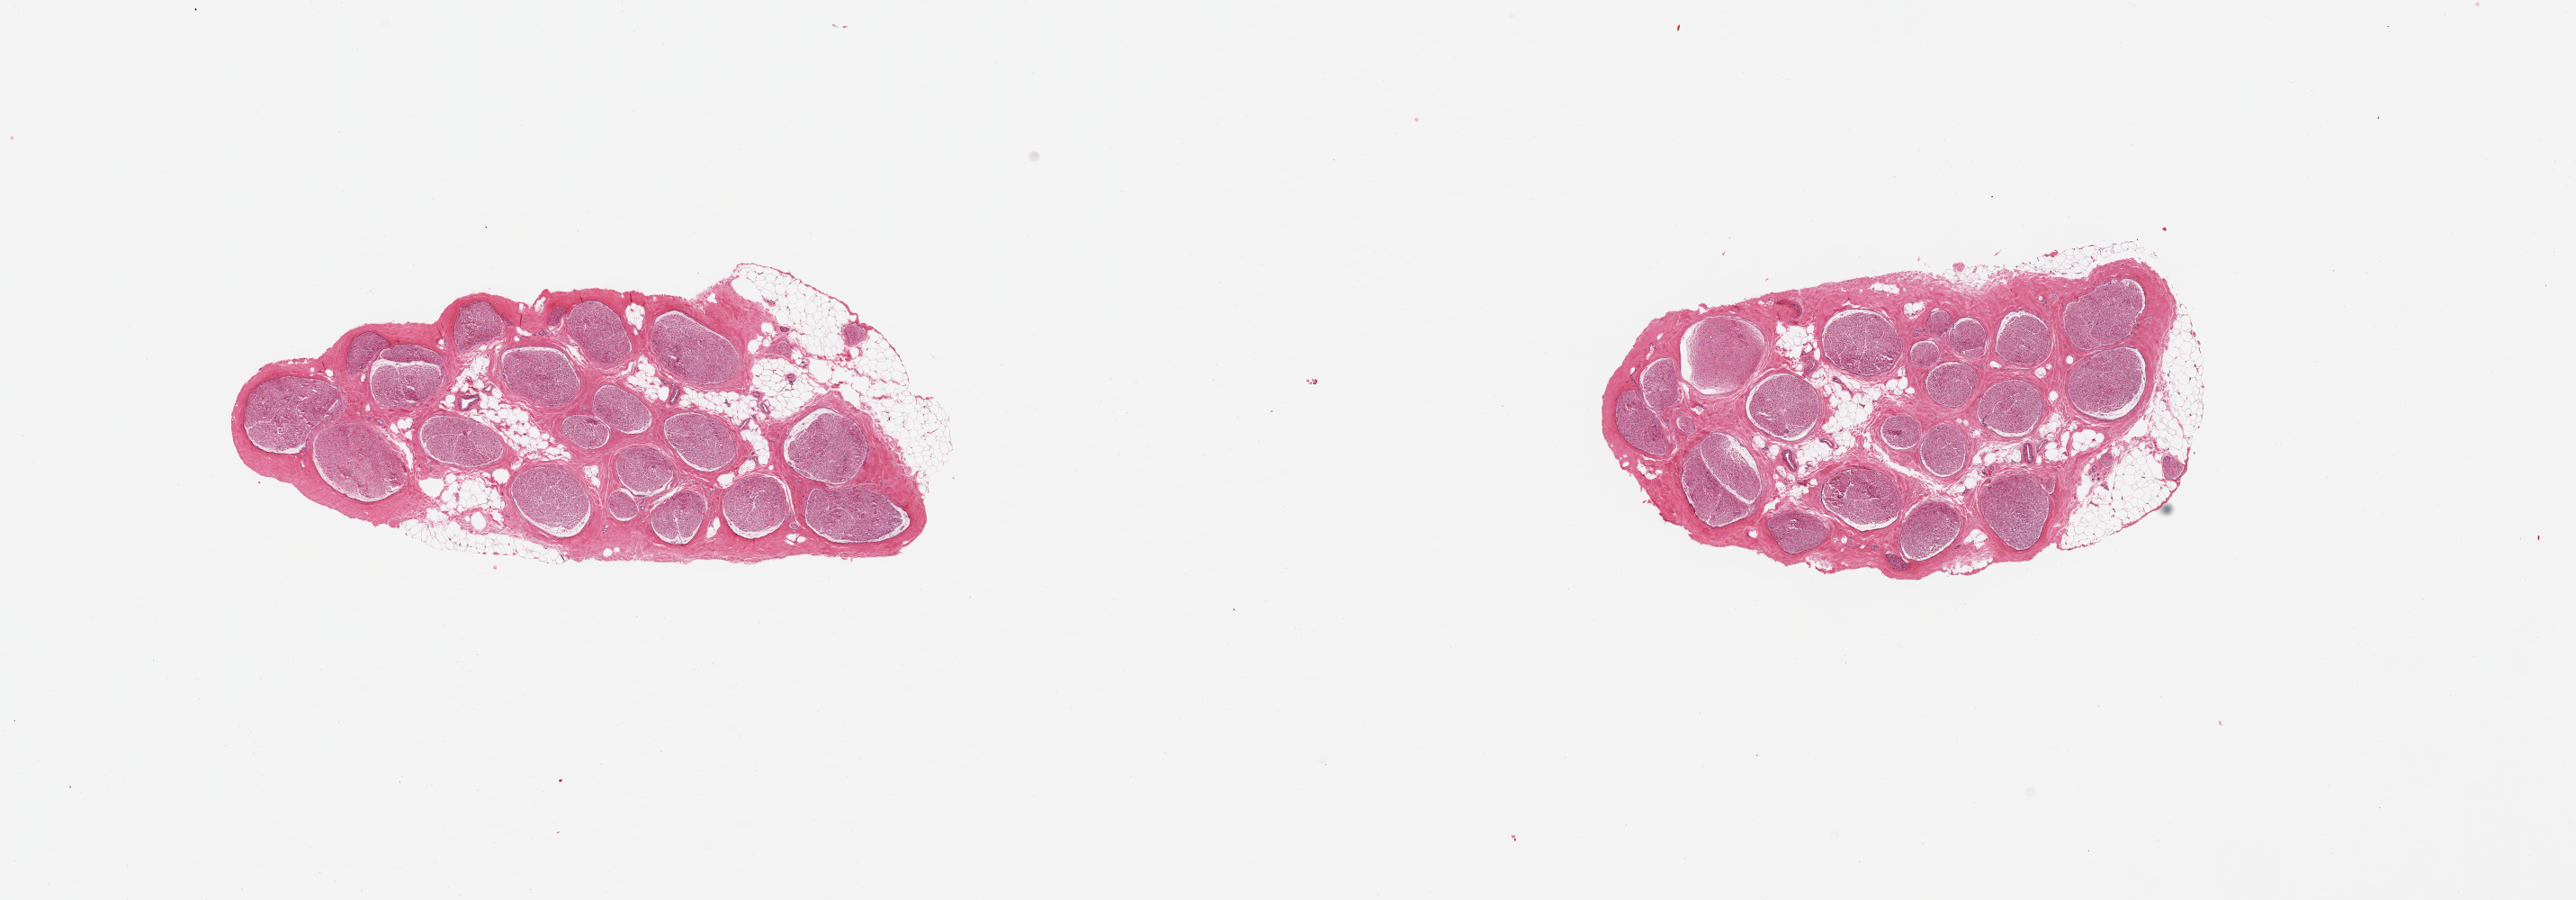
Hematoxylin and eosin (H&E) whole-slide image, whole scanned area (about 22.6 x 7.9 mm, acquisition: 20x scan) shown as a low-resolution overview. PAXgene-fixed, paraffin-embedded tissue. Sampled site (target tissue): tibial nerve. Tissue donor sample. Donor: male.
• review note (as recorded): 2 pieces, trace nubbins adherent fat, ~0.6mm